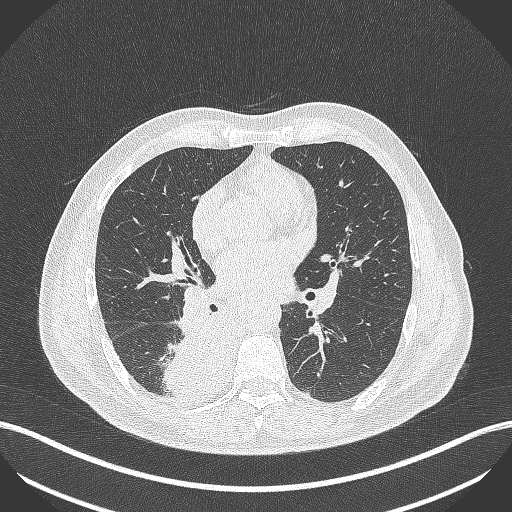
Chest CT, one axial slice. Position 239 of 451 along the scan axis. 100 kVp. Lung window (W 1500 / L -600 HU). 1 mm slice thickness. 512 × 512 image matrix, field of view 400 × 400 mm. Patient: male, 61 years. Case-level facts recorded for this patient, not image findings: clinical TNM (as recorded): T1 N0 M0; histopathological grade: G3.
Structures marked on this image (rectangle marked by the reading radiologist):
- lung tumour (recorded histology: small cell carcinoma): bounding box [x1, y1, x2, y2] px = [162, 314, 248, 400]